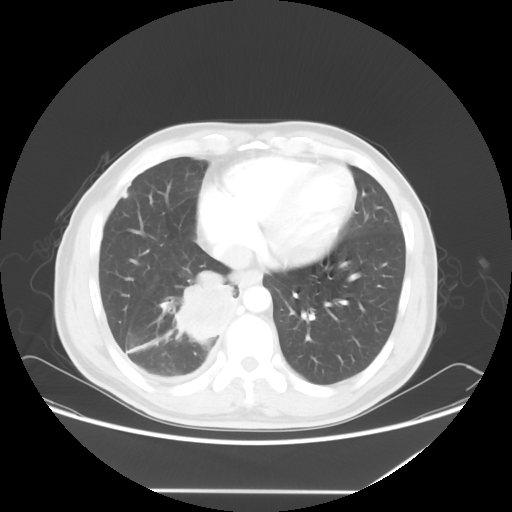
Chest CT, one axial slice; position 19 of 60 along the scan axis; reconstruction kernel STANDARD; lung window (W 1500 / L -600 HU); 512 × 512 image matrix, field of view 419 × 419 mm. Male patient, age 48 years. Case-level facts recorded for this patient, not image findings: clinical TNM (as recorded): T3 N3 M1a.
Annotated regions visible in this slice (bounding box drawn by a radiologist):
- lung tumour (recorded histology: squamous cell carcinoma): bounding box [x1, y1, x2, y2] px = [153, 264, 241, 352]